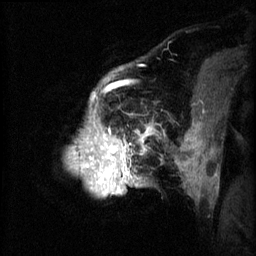
Breast MRI (dynamic contrast-enhanced), one sagittal slice; 3 images stored at this slice position (order not interpretable as contrast timing); 1.5 T; TE 4.2 ms, TR 8.2 ms; 2.3 mm slice thickness; 256 × 256 image matrix. Female patient, age 50 years.
Structures marked on this image (semi-automatic segmentation, software-assisted and operator-edited):
- analysis volume of interest (the breast-tissue region the enhancement analysis was run in; not a lesion): bounding box (x1, y1, x2, y2) in pixels: (68, 64, 169, 199)
- tumour enhancement mask (voxels above the 70 % enhancement threshold inside the analysis volume of interest): (70, 84, 153, 191)